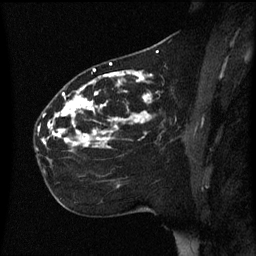
Breast MRI (dynamic contrast-enhanced), one sagittal slice. Dynamic contrast-enhanced series, image 2 of 3 at this slice position (ordered by acquisition). 1.5 T. TE 4.2 ms, TR 8.4 ms. 2.2 mm slice thickness. 256 × 256 image matrix. Female patient, age 35 years. From the clinical record (not read from this slice): setting: breast cancer imaged before/during neoadjuvant chemotherapy; receptor status: HER2-positive.
Annotated regions visible in this slice (semi-automatic segmentation, software-assisted and operator-edited):
- analysis volume of interest (the breast-tissue region the enhancement analysis was run in; not a lesion): box from (x=35, y=78) to (x=173, y=163) px
- tumour enhancement mask (voxels above the 70 % enhancement threshold inside the analysis volume of interest): (x=42, y=78)–(x=152, y=149)